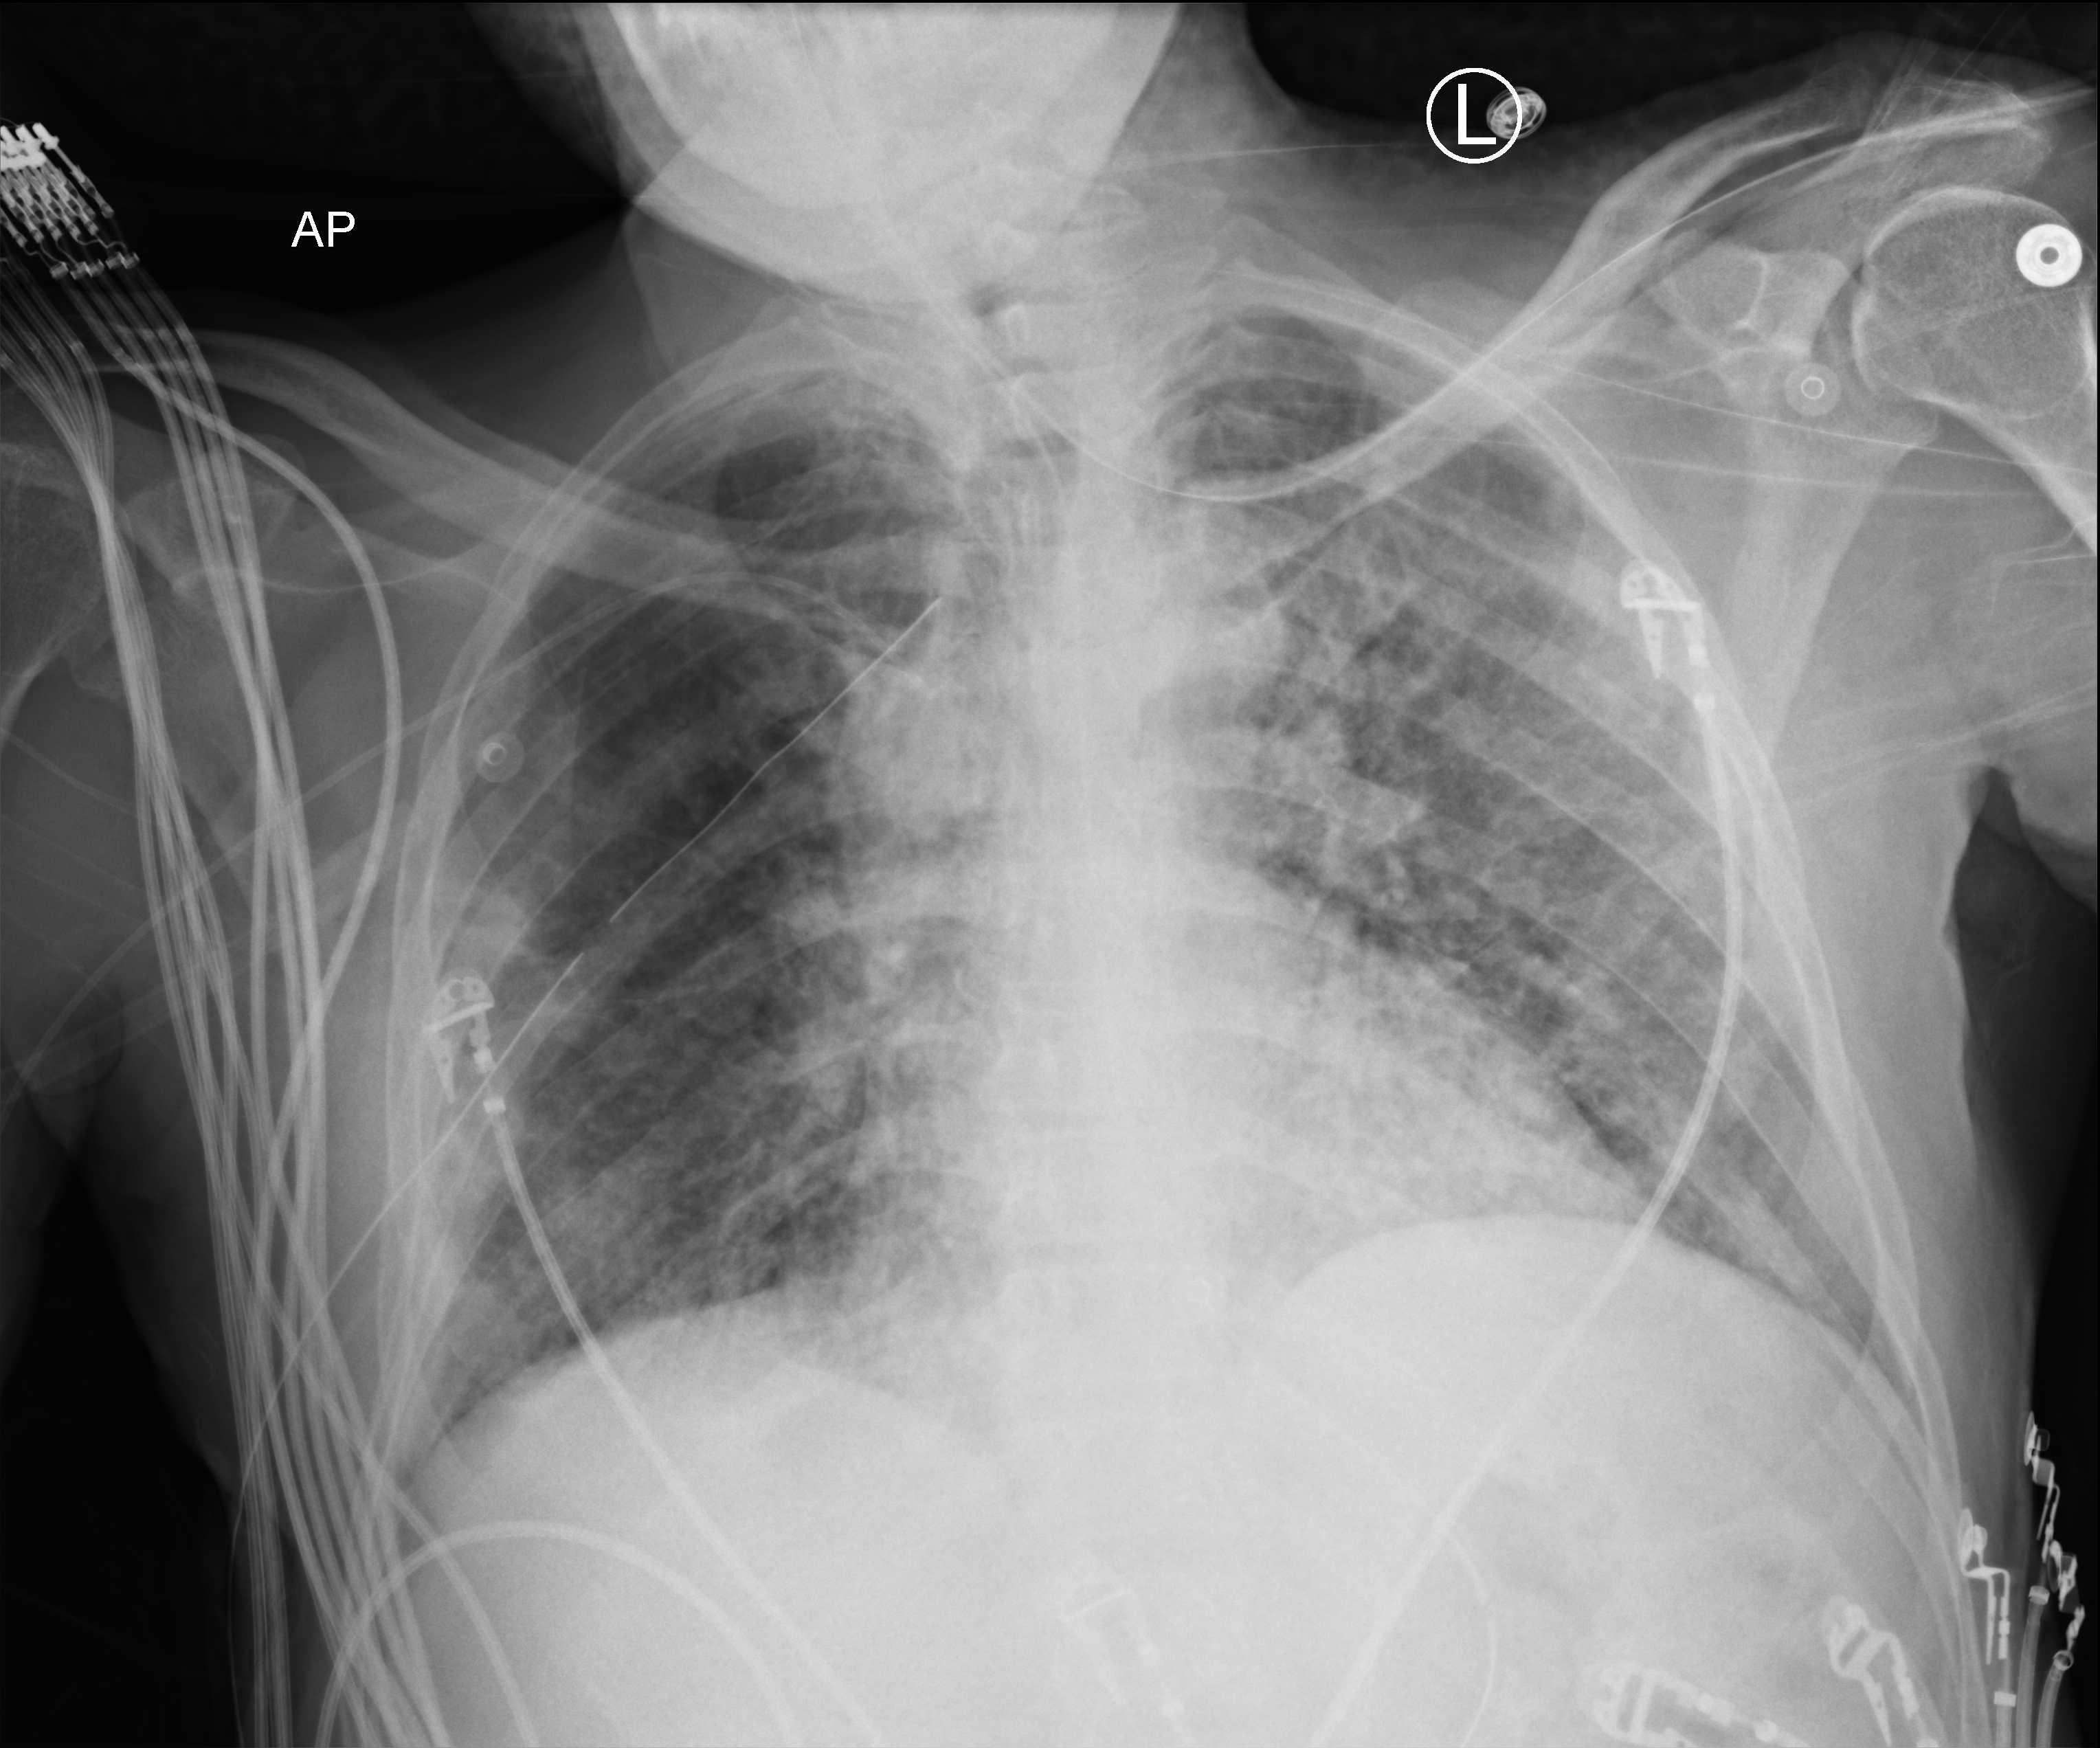
Portable chest radiograph, anteroposterior (AP) projection. Patient hospitalised with COVID-19; male, aged 18–59 years.
Admission-level facts for this patient (not findings on this image; timing relative to this image not recorded):
- admitted to intensive care during this hospital stay: yes
- diabetes (admission record): yes